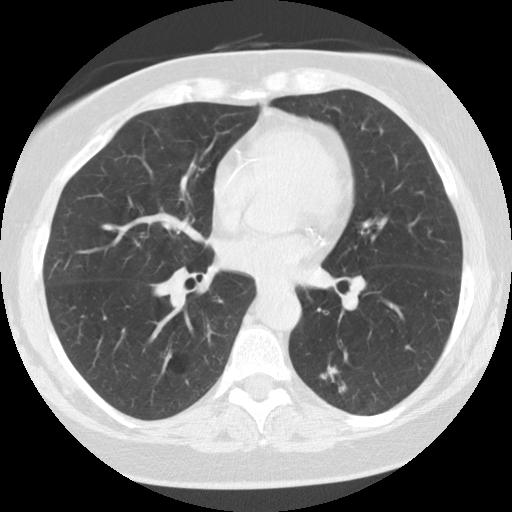
Chest CT (low-dose screening protocol), one axial image, baseline screening round, lung window (W 1500 / L -600 HU), 2.5 mm slice thickness, standard (soft-tissue) reconstruction kernel (STANDARD), 512 × 512 image matrix. Female, age 59 years at enrolment.
- Lesion marked by an expert reader, bounding box [x1, y1, x2, y2] px = [293, 351, 363, 416].
- The screening reader recorded 5 non-calcified nodules or masses ≥4 mm on this exam (right upper lobe, right lower lobe, left lower lobe, right lower lobe, left lower lobe); which of them this box marks is not recorded.
- Official screen result: positive, change unspecified: nodule(s) >= 4 mm or enlarging nodule(s), mass(es), or other non-specific abnormalities suspicious for lung cancer.
- Lung cancer was diagnosed 707 days after this screen: adenocarcinoma, NOS, left lower lobe, poorly differentiated (G3), stage IA (AJCC 6th edition), 15 mm at pathology.